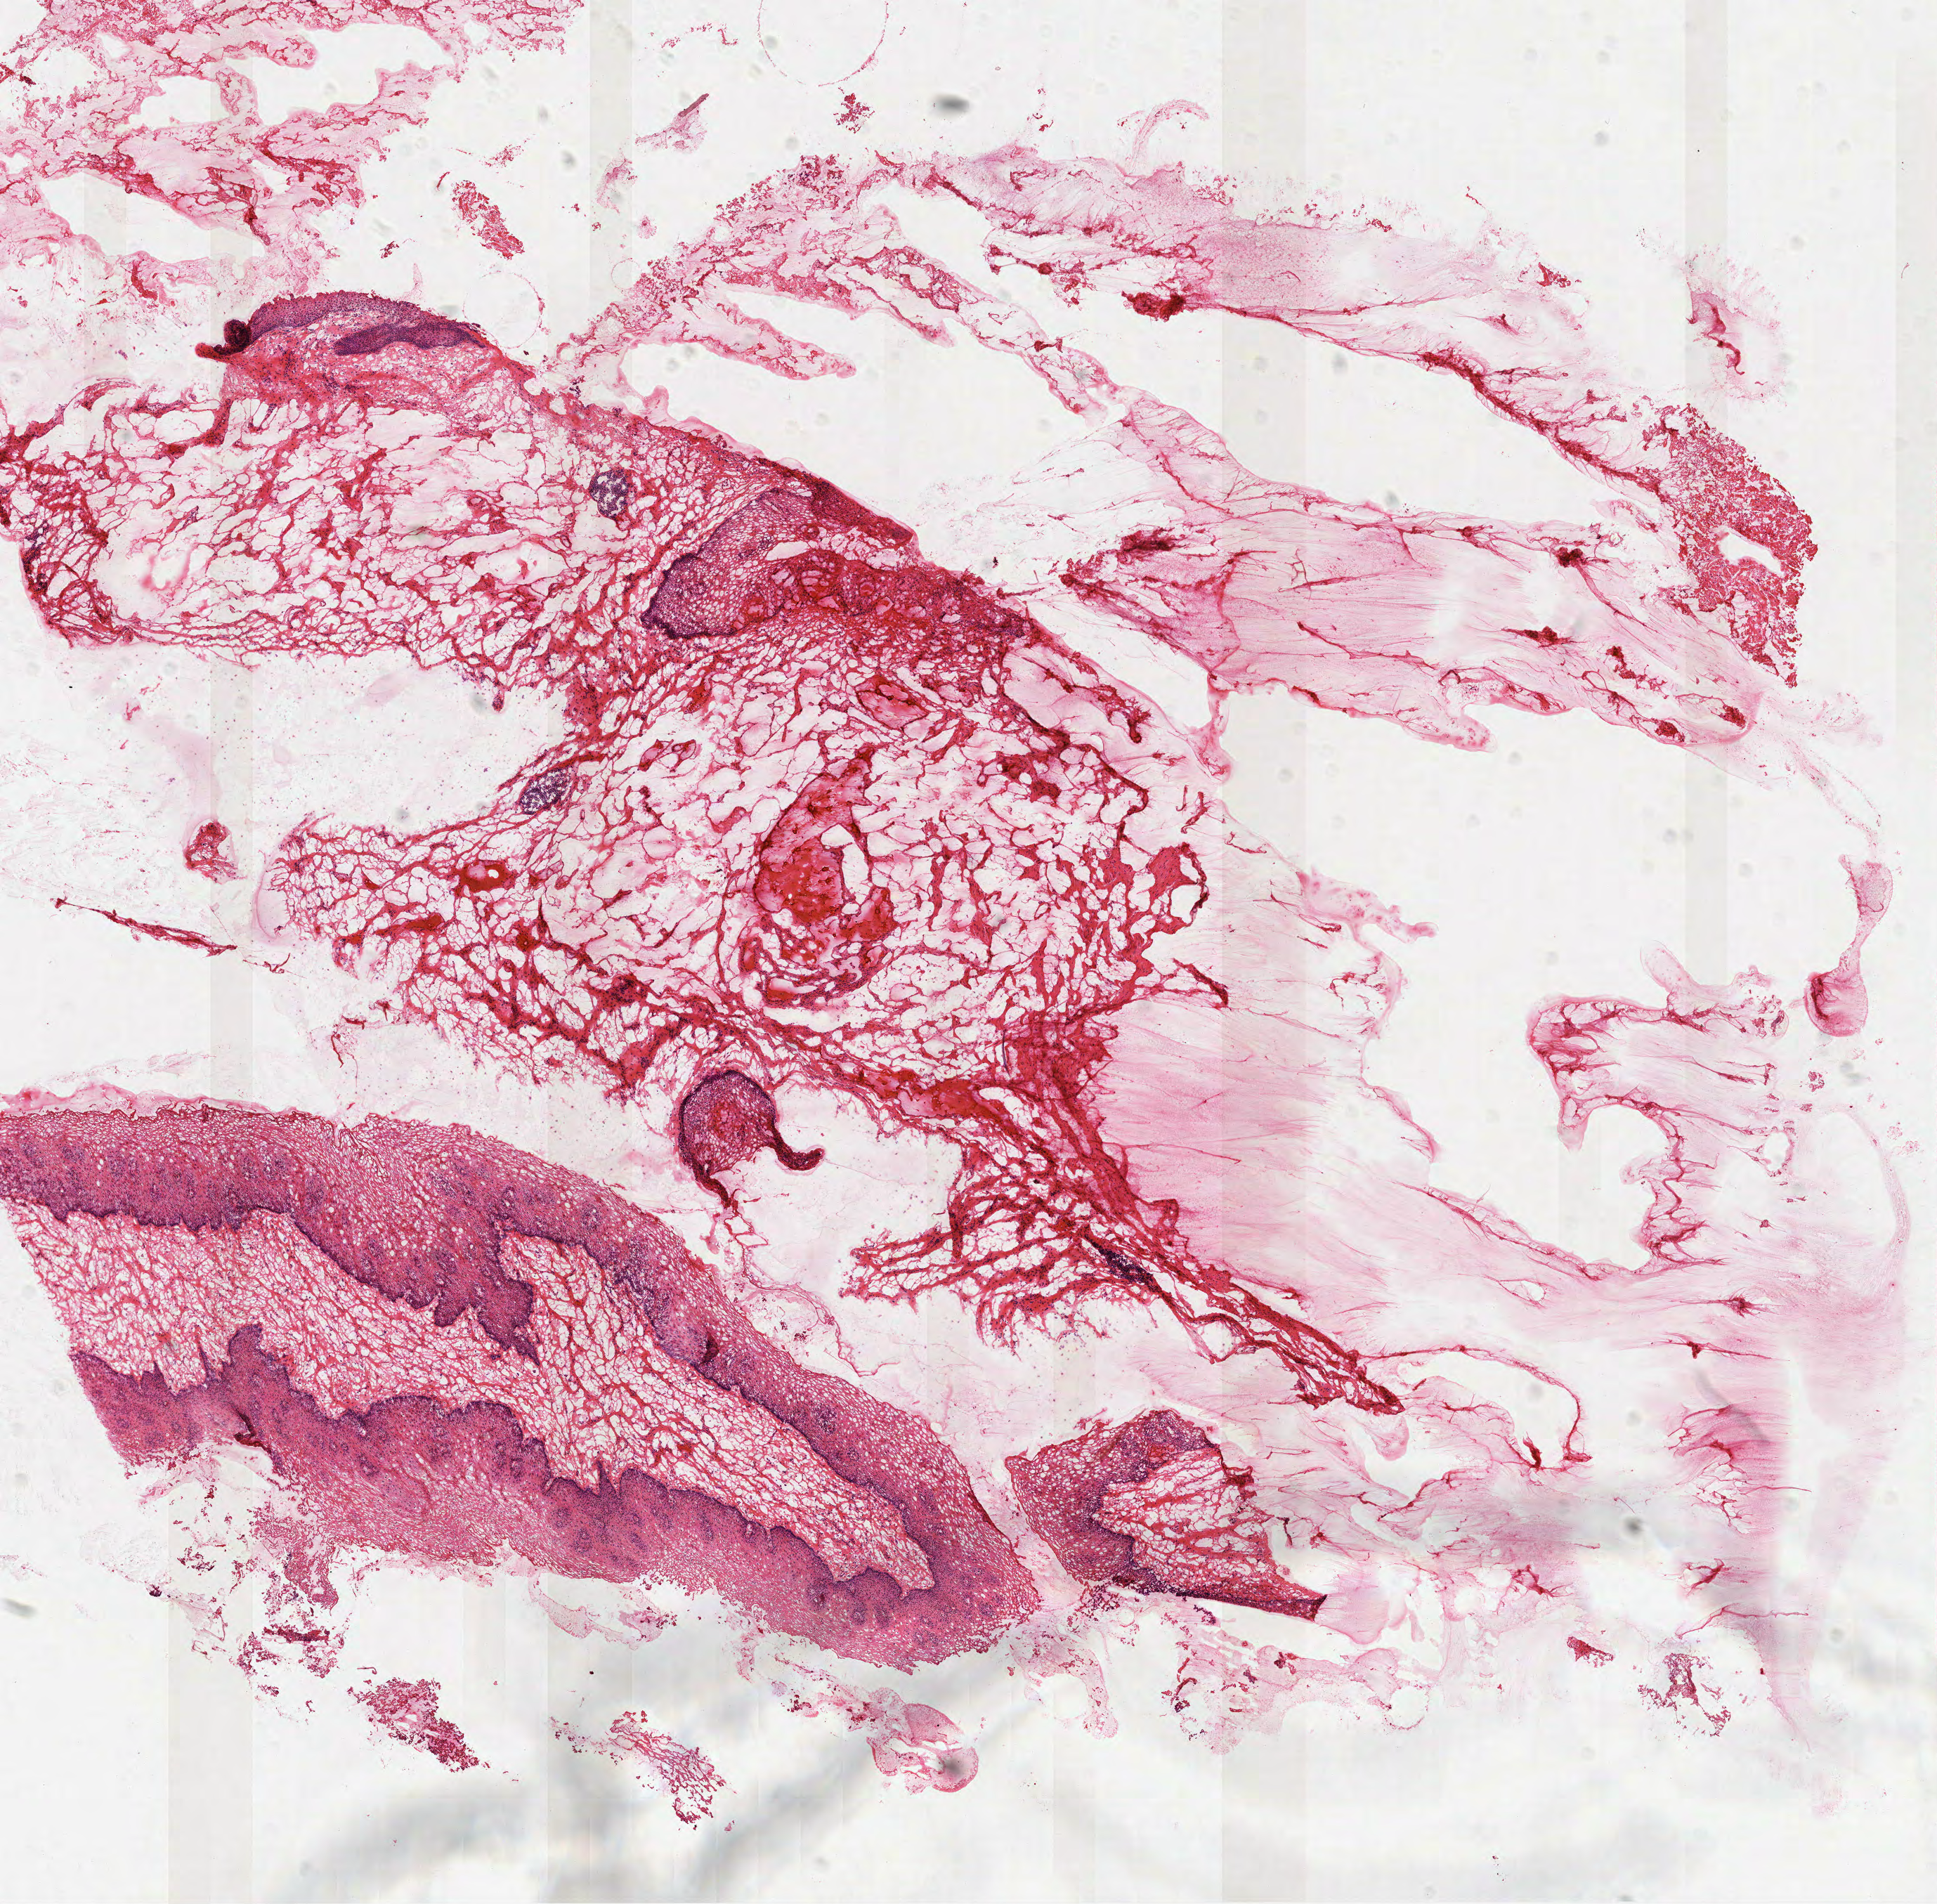
Digitized Hematoxylin and eosin (H&E) stained tissue section (whole slide) — a low-resolution overview of the entire scanned area, about 11.1 x 10.9 mm (slide scanned at 40x). Frozen section from the top of the tissue portion. Sample: solid tissue normal (non-tumour tissue), stomach. Male patient; age at initial diagnosis 80 years.
This section: solid tissue normal sample (biorepository sample class). Patient diagnosis: Adenocarcinoma, NOS (cardia, NOS).